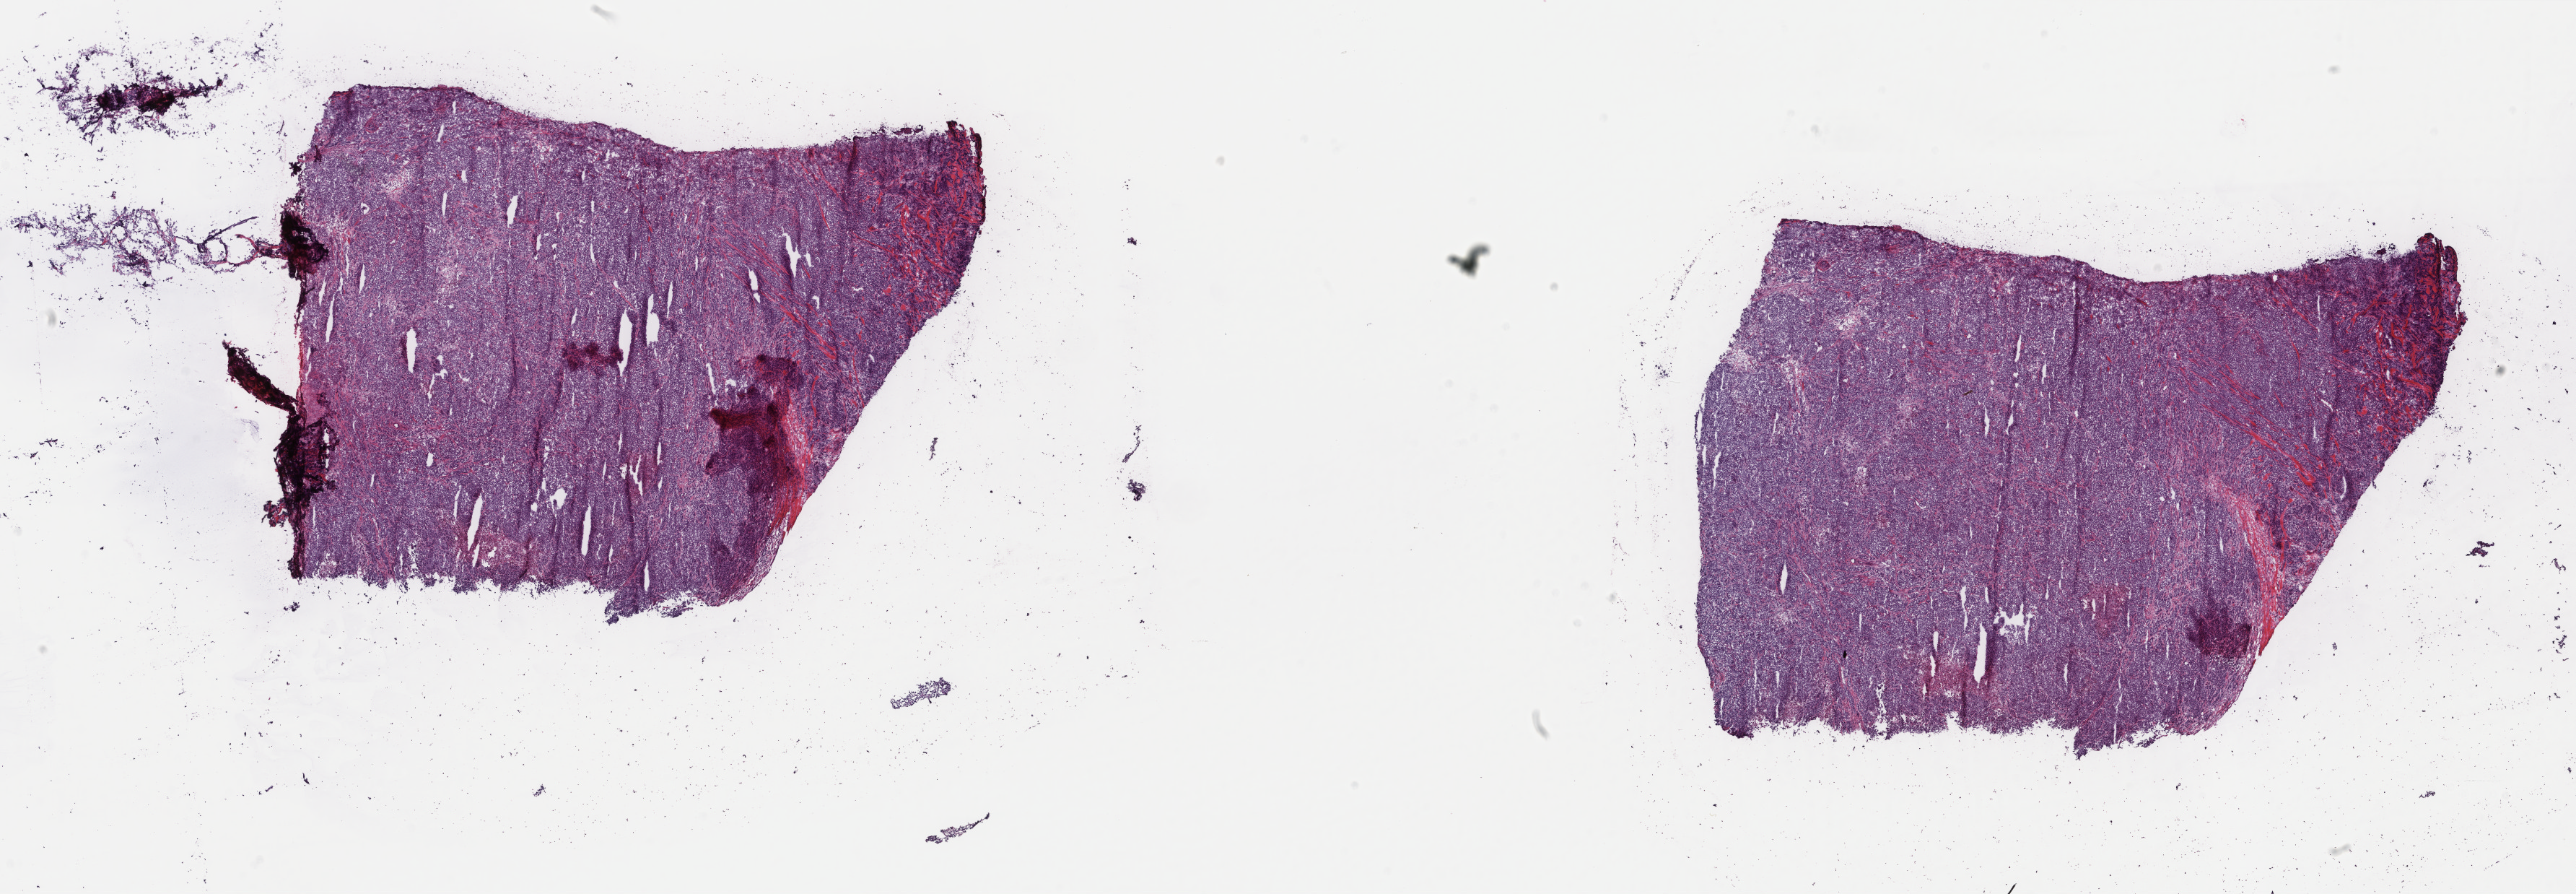
Digitized Hematoxylin and eosin (H&E) stained tissue section (whole slide) — whole scanned area (about 28.3 x 9.8 mm) shown as a low-resolution overview. Frozen section from the top of the tissue portion. Breast, primary tumour sample. Female patient; age at initial diagnosis 51 years. Pathologist review of this section (percent, as recorded): tumour cells 100%, tumour nuclei 95%, normal cells 0%, stromal cells 0%, necrosis 0%. Infiltration values recorded for this section: lymphocyte infiltration 0%, monocyte infiltration 0%, neutrophil infiltration 0%.
Histologic diagnosis: Infiltrating duct carcinoma, NOS. Laterality: right. AJCC pathologic stage: IIB (6th edition). Lymph nodes positive (case pathology): 1 of 9 examined.